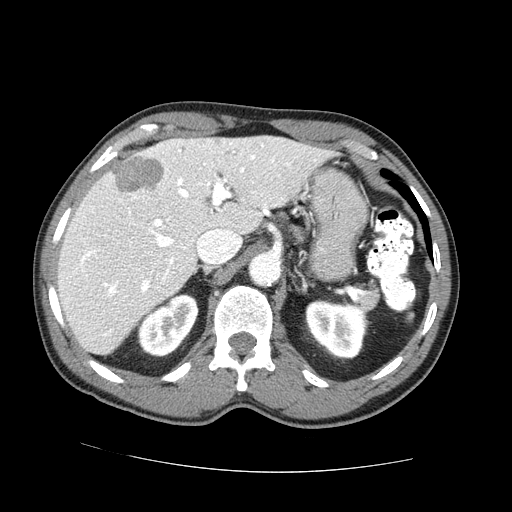
Contrast-enhanced abdominal CT (liver protocol), one axial slice; slice 48 of 73 in the series (ordered by position); 100 kVp; one of 2 acquisitions stored at this slice position; soft-tissue window (W 400 / L 40 HU); 512 × 512 image matrix, field of view 380 × 380 mm. Case-level facts recorded for this patient, not image findings: diagnosis: hepatocellular carcinoma (patient treated with transarterial chemoembolisation; whether this scan precedes or follows treatment is not stated here); TNM stage (as recorded): Stage-IVA; Child-Pugh class: A; tumour differentiation: no biopsy.
Annotated regions visible in this slice (semi-automatic segmentation, software-assisted and operator-edited):
- liver parenchyma outside the tumour (the mass and vessels are separate outlines, so this box may not span the whole liver): bounding box (x1, y1, x2, y2) in pixels: (58, 136, 332, 354)
- mass: (112, 156, 163, 192)
- liver vessels: (81, 142, 290, 336)